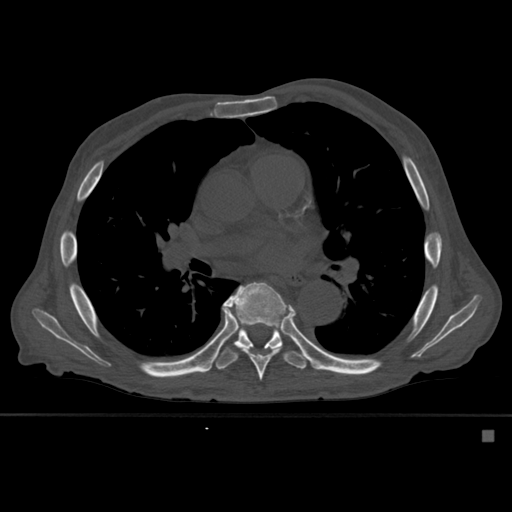
CT including the spine, one axial slice; slice 360 of 527 in the series (ordered by position); bone window (W 1800 / L 400 HU); 1.5 mm slice thickness; 512 × 512 image matrix, field of view 373 × 373 mm. Patient: male, 78 years. From the clinical record (not read from this slice): primary cancer: prostate.
Annotated regions visible in this slice (semi-automatically segmented with operator editing):
- T7 vertebra: bounding box [x1, y1, x2, y2] px = [222, 282, 296, 381]
- T8 vertebra: [215, 323, 308, 370]